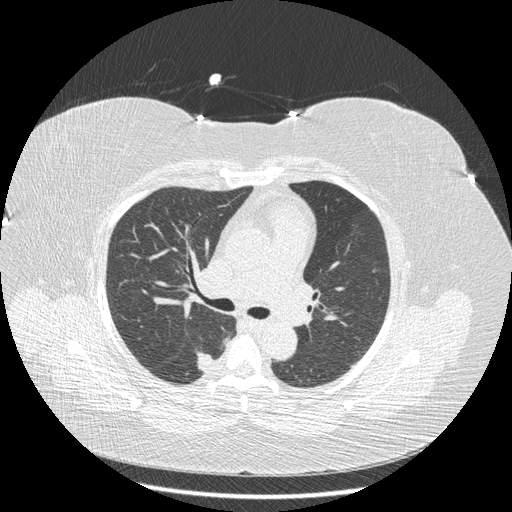
Axial slice from a low-dose chest CT screening exam, first (baseline) screen, lung window (W 1500 / L -600 HU), 1.25 mm slice thickness, slice 79 of 211 in the series. Female, age 58 years at enrolment. Current smoker at enrolment.
Lesion marked by an expert reader, bounding box <185,345,226,382> (left, top, right, bottom; pixels). The exam's reader record, not a measurement of the box and not confirmed to be the same lesion: non-calcified nodule or mass ≥4 mm, right lower lobe, 15 × 10 mm, smooth margins, soft tissue attenuation. Official screen result: positive, change unspecified: nodule(s) >= 4 mm or enlarging nodule(s), mass(es), or other non-specific abnormalities suspicious for lung cancer. Later outcome: lung cancer diagnosed 362 days after this screen (after the second annual screen) — adenocarcinoma, NOS, right lower lobe, stage IB (AJCC 6th edition), 15 mm at pathology.